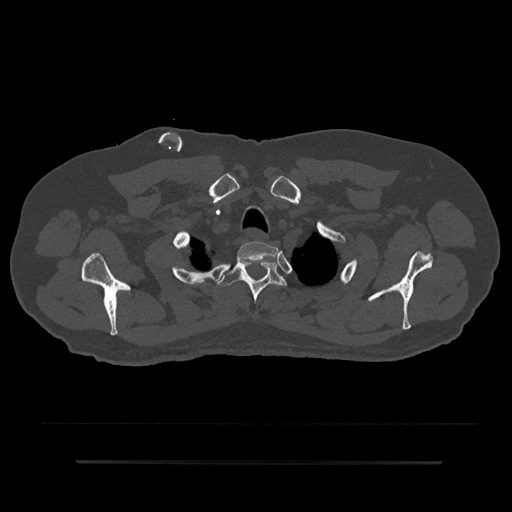
CT including the spine, one axial slice; slice 708 of 797 in the series (ordered by position); 120 kVp; bone window (W 1800 / L 400 HU); 0.5 mm slice thickness; 512 × 512 image matrix, field of view 464 × 464 mm. Patient: male, 59 years. From the clinical record (not read from this slice): primary cancer: bile ducts; vertebrae with lytic lesions (as recorded): T10.
Outlined on this slice (semi-automatic segmentation, software-assisted and operator-edited):
- T1 vertebra: bounding box <237,241,278,263> (left, top, right, bottom; pixels)
- T2 vertebra: <217,258,288,304>